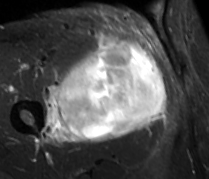
MRI of an extremity soft-tissue mass, one axial slice; position 44 of 89 along the scan axis; STIR; MR volume resampled by the dataset authors to the PET/CT grid (not the native acquisition matrix); 3.27 mm slice thickness; 209 × 179 image matrix, field of view 204 × 175 mm. Male patient. From the clinical record (not read from this slice): histological type: undifferentiated - pleiomorphic; grade: high; site of the primary tumour: right thigh.
Outlined on this slice (expert contour drawn on MRI and transferred to this co-registered scan by the dataset authors):
- gross tumour volume including surrounding oedema: bounding box [x1, y1, x2, y2] px = [41, 39, 166, 145]
- gross tumour volume (mass): [55, 39, 166, 140]